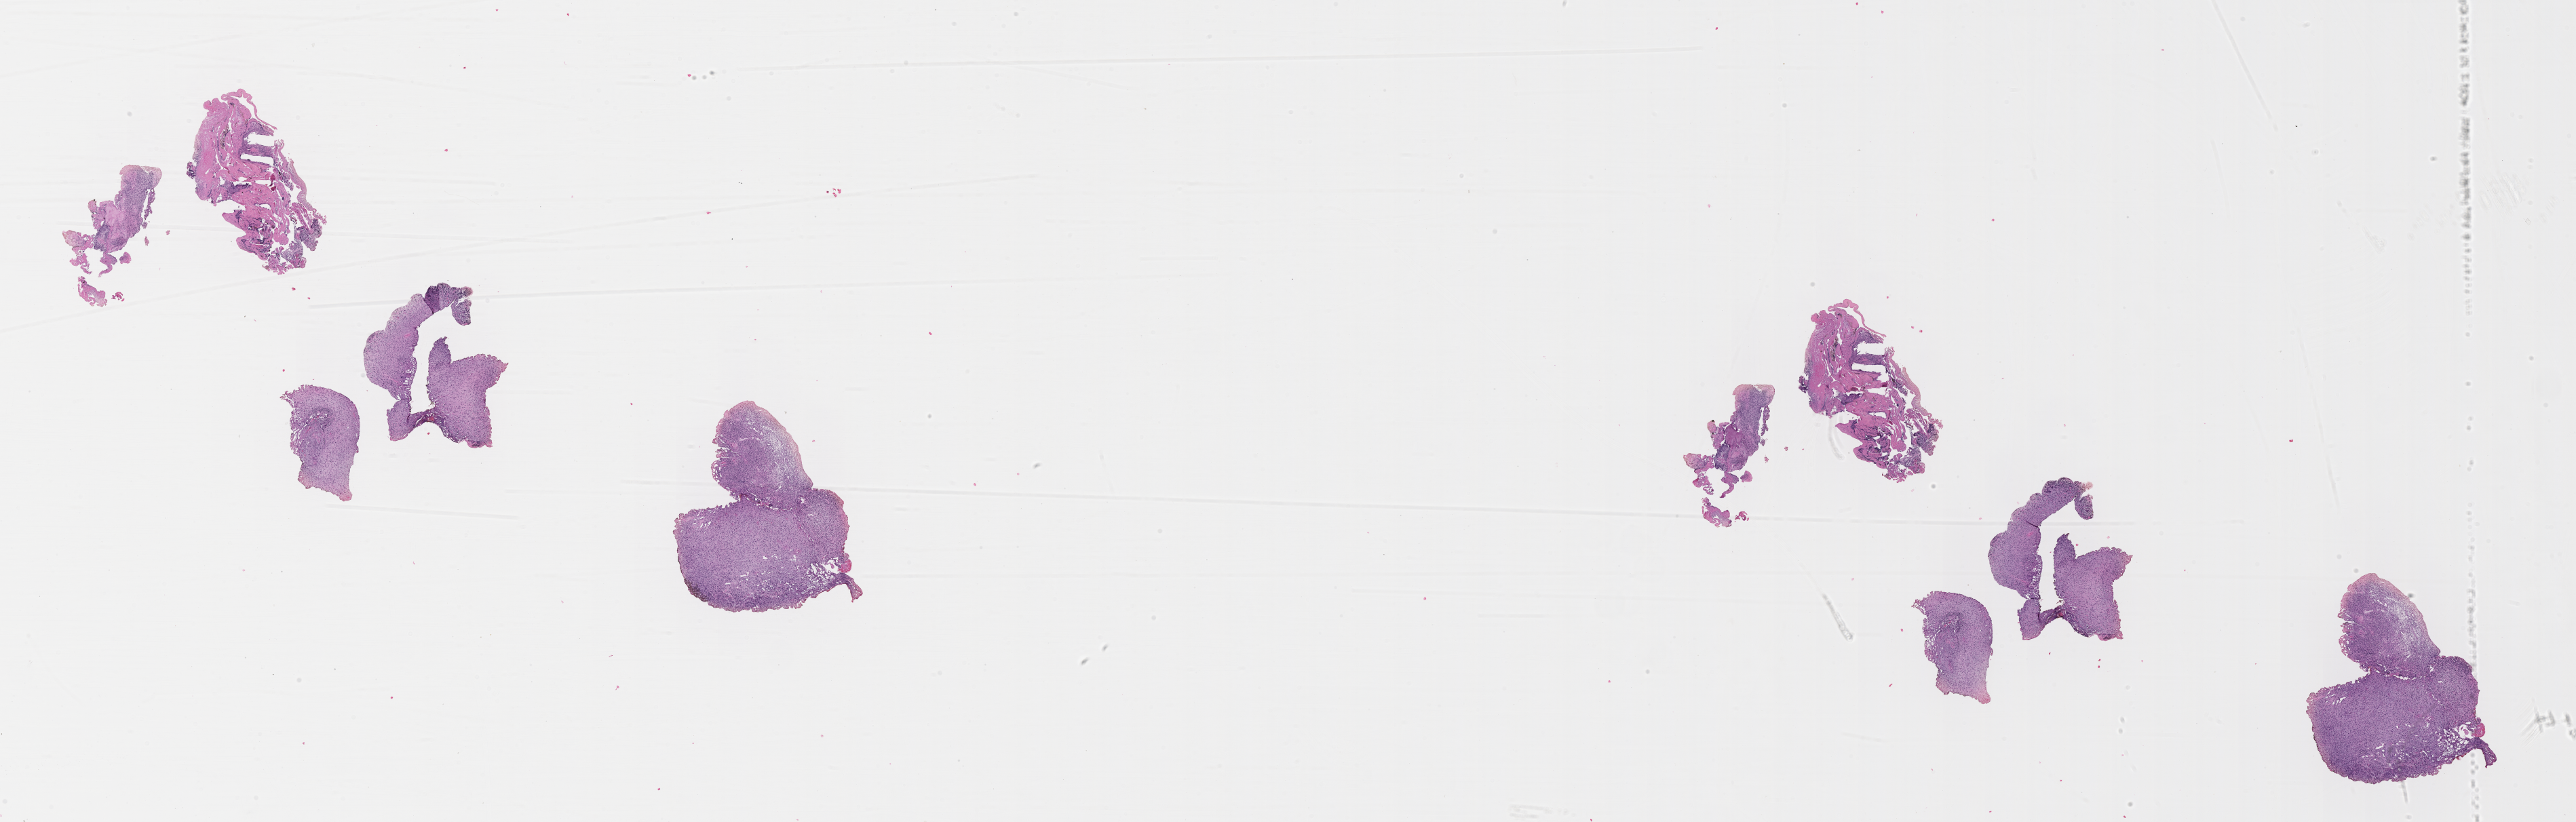
H&E whole-slide image of tumor tissue, shown as a low-resolution overview of the whole scanned area (about 30.7 x 9.8 mm). FFPE section. Sample anatomic site: bladder. Male patient, age at diagnosis 1.7 years.
Stage (as recorded): 1. Diagnosis: rhabdomyosarcoma; histological classification: embryonal rhabdomyosarcoma. Metastatic status at presentation (as recorded): non-metastatic (confirmed).